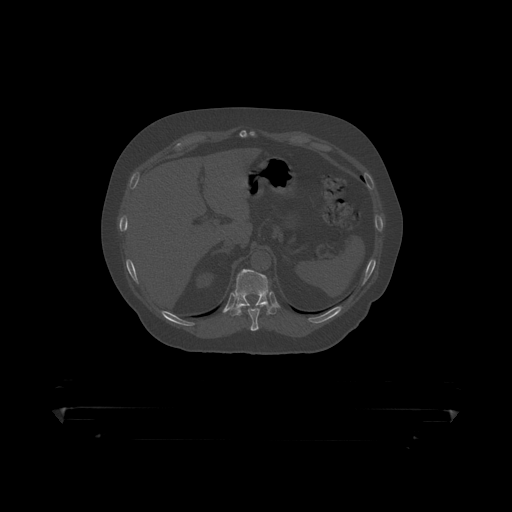
CT including the spine, one axial slice. Slice 203 of 390 in the series (ordered by position). Reconstruction kernel STANDARD. Bone window (W 1800 / L 400 HU). 1.25 mm slice thickness. 512 × 512 image matrix, field of view 650 × 650 mm. Patient: male, 60 years. From the clinical record (not read from this slice): primary cancer: prostate.
Annotated regions visible in this slice (semi-automatically segmented with operator editing):
- T10 vertebra: bounding box <240,304,267,319> (left, top, right, bottom; pixels)
- T11 vertebra: <227,270,278,316>